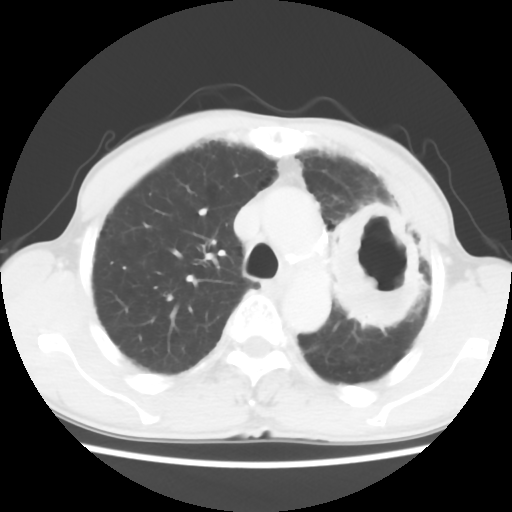
Chest CT, one axial slice. Slice 43 of 60 in the series (ordered by position). Lung window (W 1500 / L -600 HU). 512 × 512 image matrix. Male patient, age 64 years. From the clinical record (not read from this slice): clinical TNM (as recorded): T3 N3 M0.
Annotated regions visible in this slice (bounding box drawn by a radiologist):
- lung tumour (recorded histology: adenocarcinoma): bounding box (x1, y1, x2, y2) in pixels: (328, 192, 435, 346)